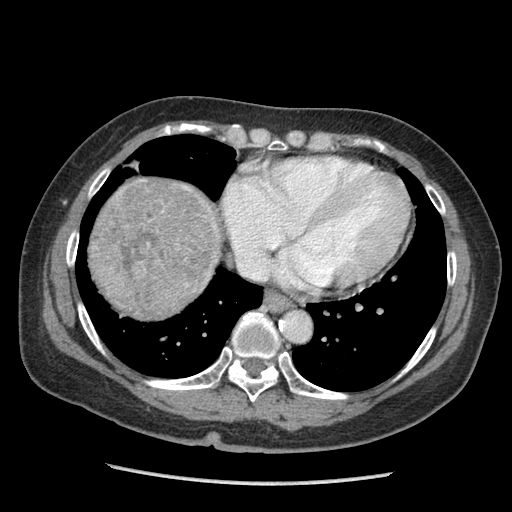
Contrast-enhanced abdominal CT (liver protocol), one axial slice; position 90 of 105 along the scan axis; reconstruction kernel STANDARD; soft-tissue window (W 400 / L 40 HU); 2.5 mm slice thickness; 512 × 512 image matrix, field of view 340 × 340 mm. From the clinical record (not read from this slice): diagnosis: hepatocellular carcinoma (patient treated with transarterial chemoembolisation; whether this scan precedes or follows treatment is not stated here); TNM stage (as recorded): Stage-I; Child-Pugh class: A; tumour differentiation: moderately differentiated; tumour nodularity: uninodular.
Annotated regions visible in this slice (semi-automatically segmented with operator editing):
- liver parenchyma outside the tumour (the mass and vessels are separate outlines, so this box may not span the whole liver): bounding box [x1, y1, x2, y2] px = [88, 176, 218, 318]
- mass: [93, 181, 223, 318]